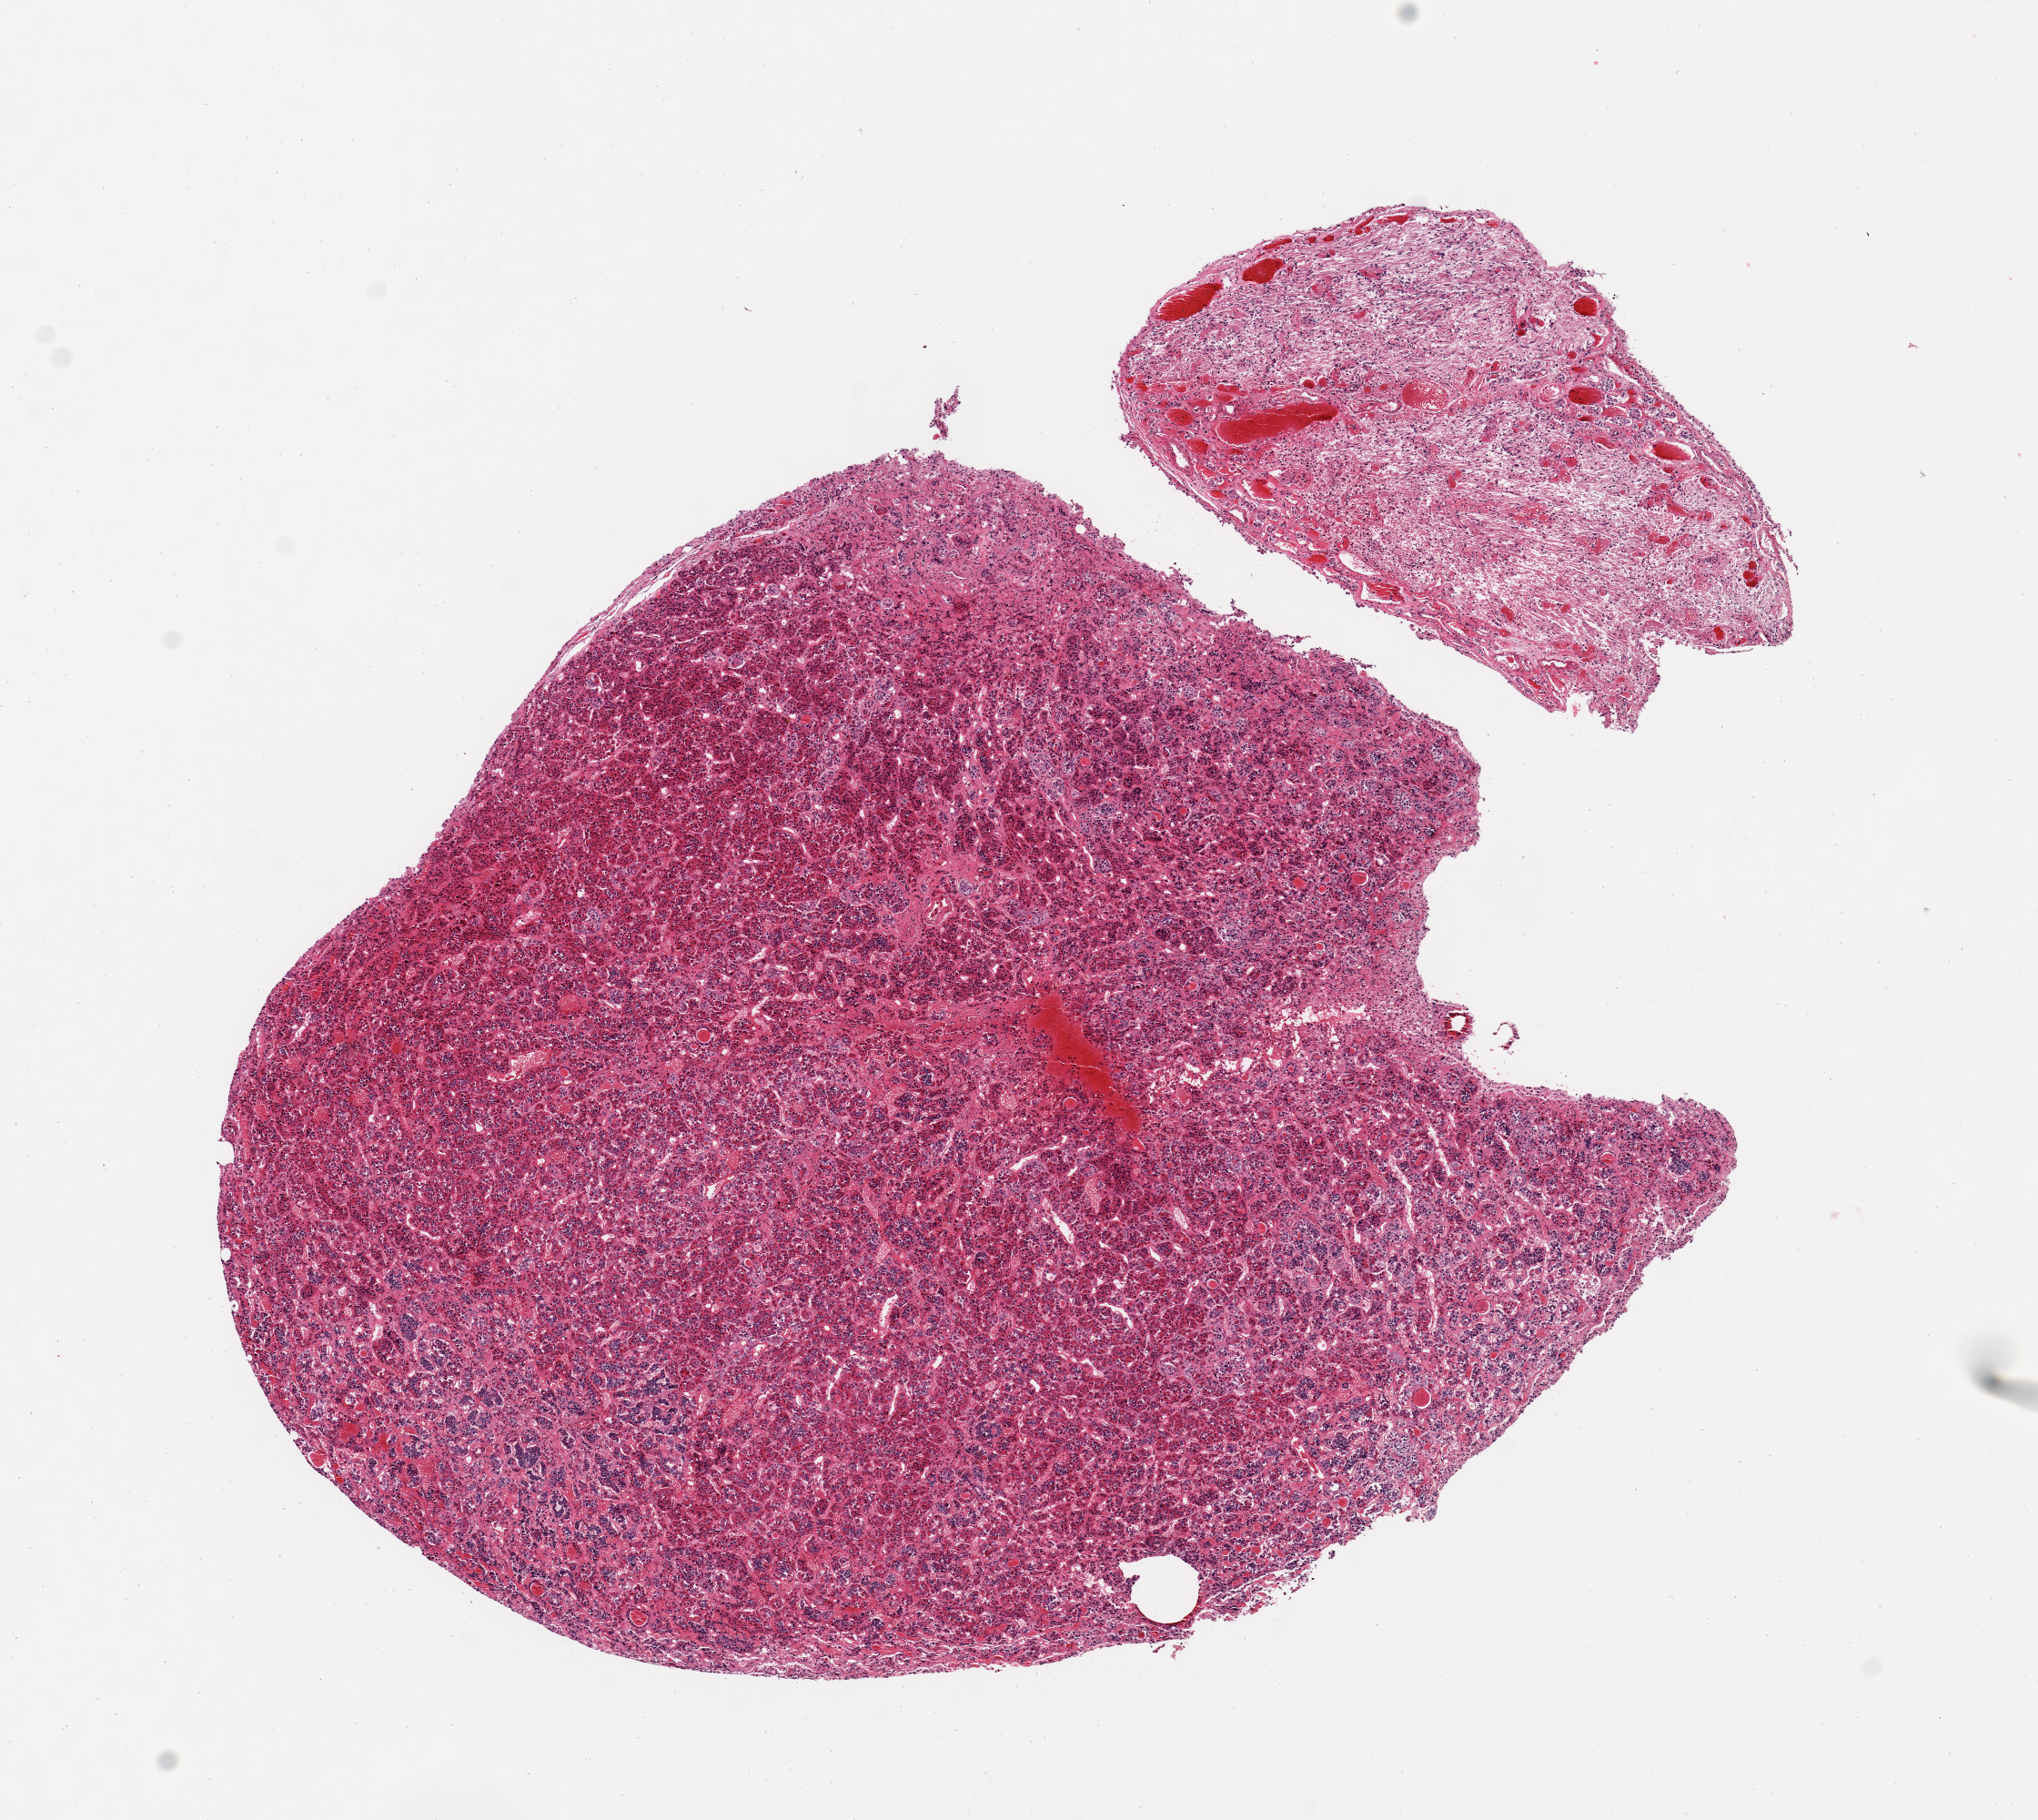
Hematoxylin and eosin (H&E) whole-slide image, shown as a low-resolution overview of the whole scanned area (about 8.9 x 7.9 mm, from a 20x scan), PAXgene-fixed paraffin-embedded (PFPE) section, sampled site (target tissue): pituitary, tissue donor sample. Donor: female.
Pathologist's review note for this sample: 2 pieces, larger is adenohypophysis; smaller is 2.5mm piece of neurohypophysis.